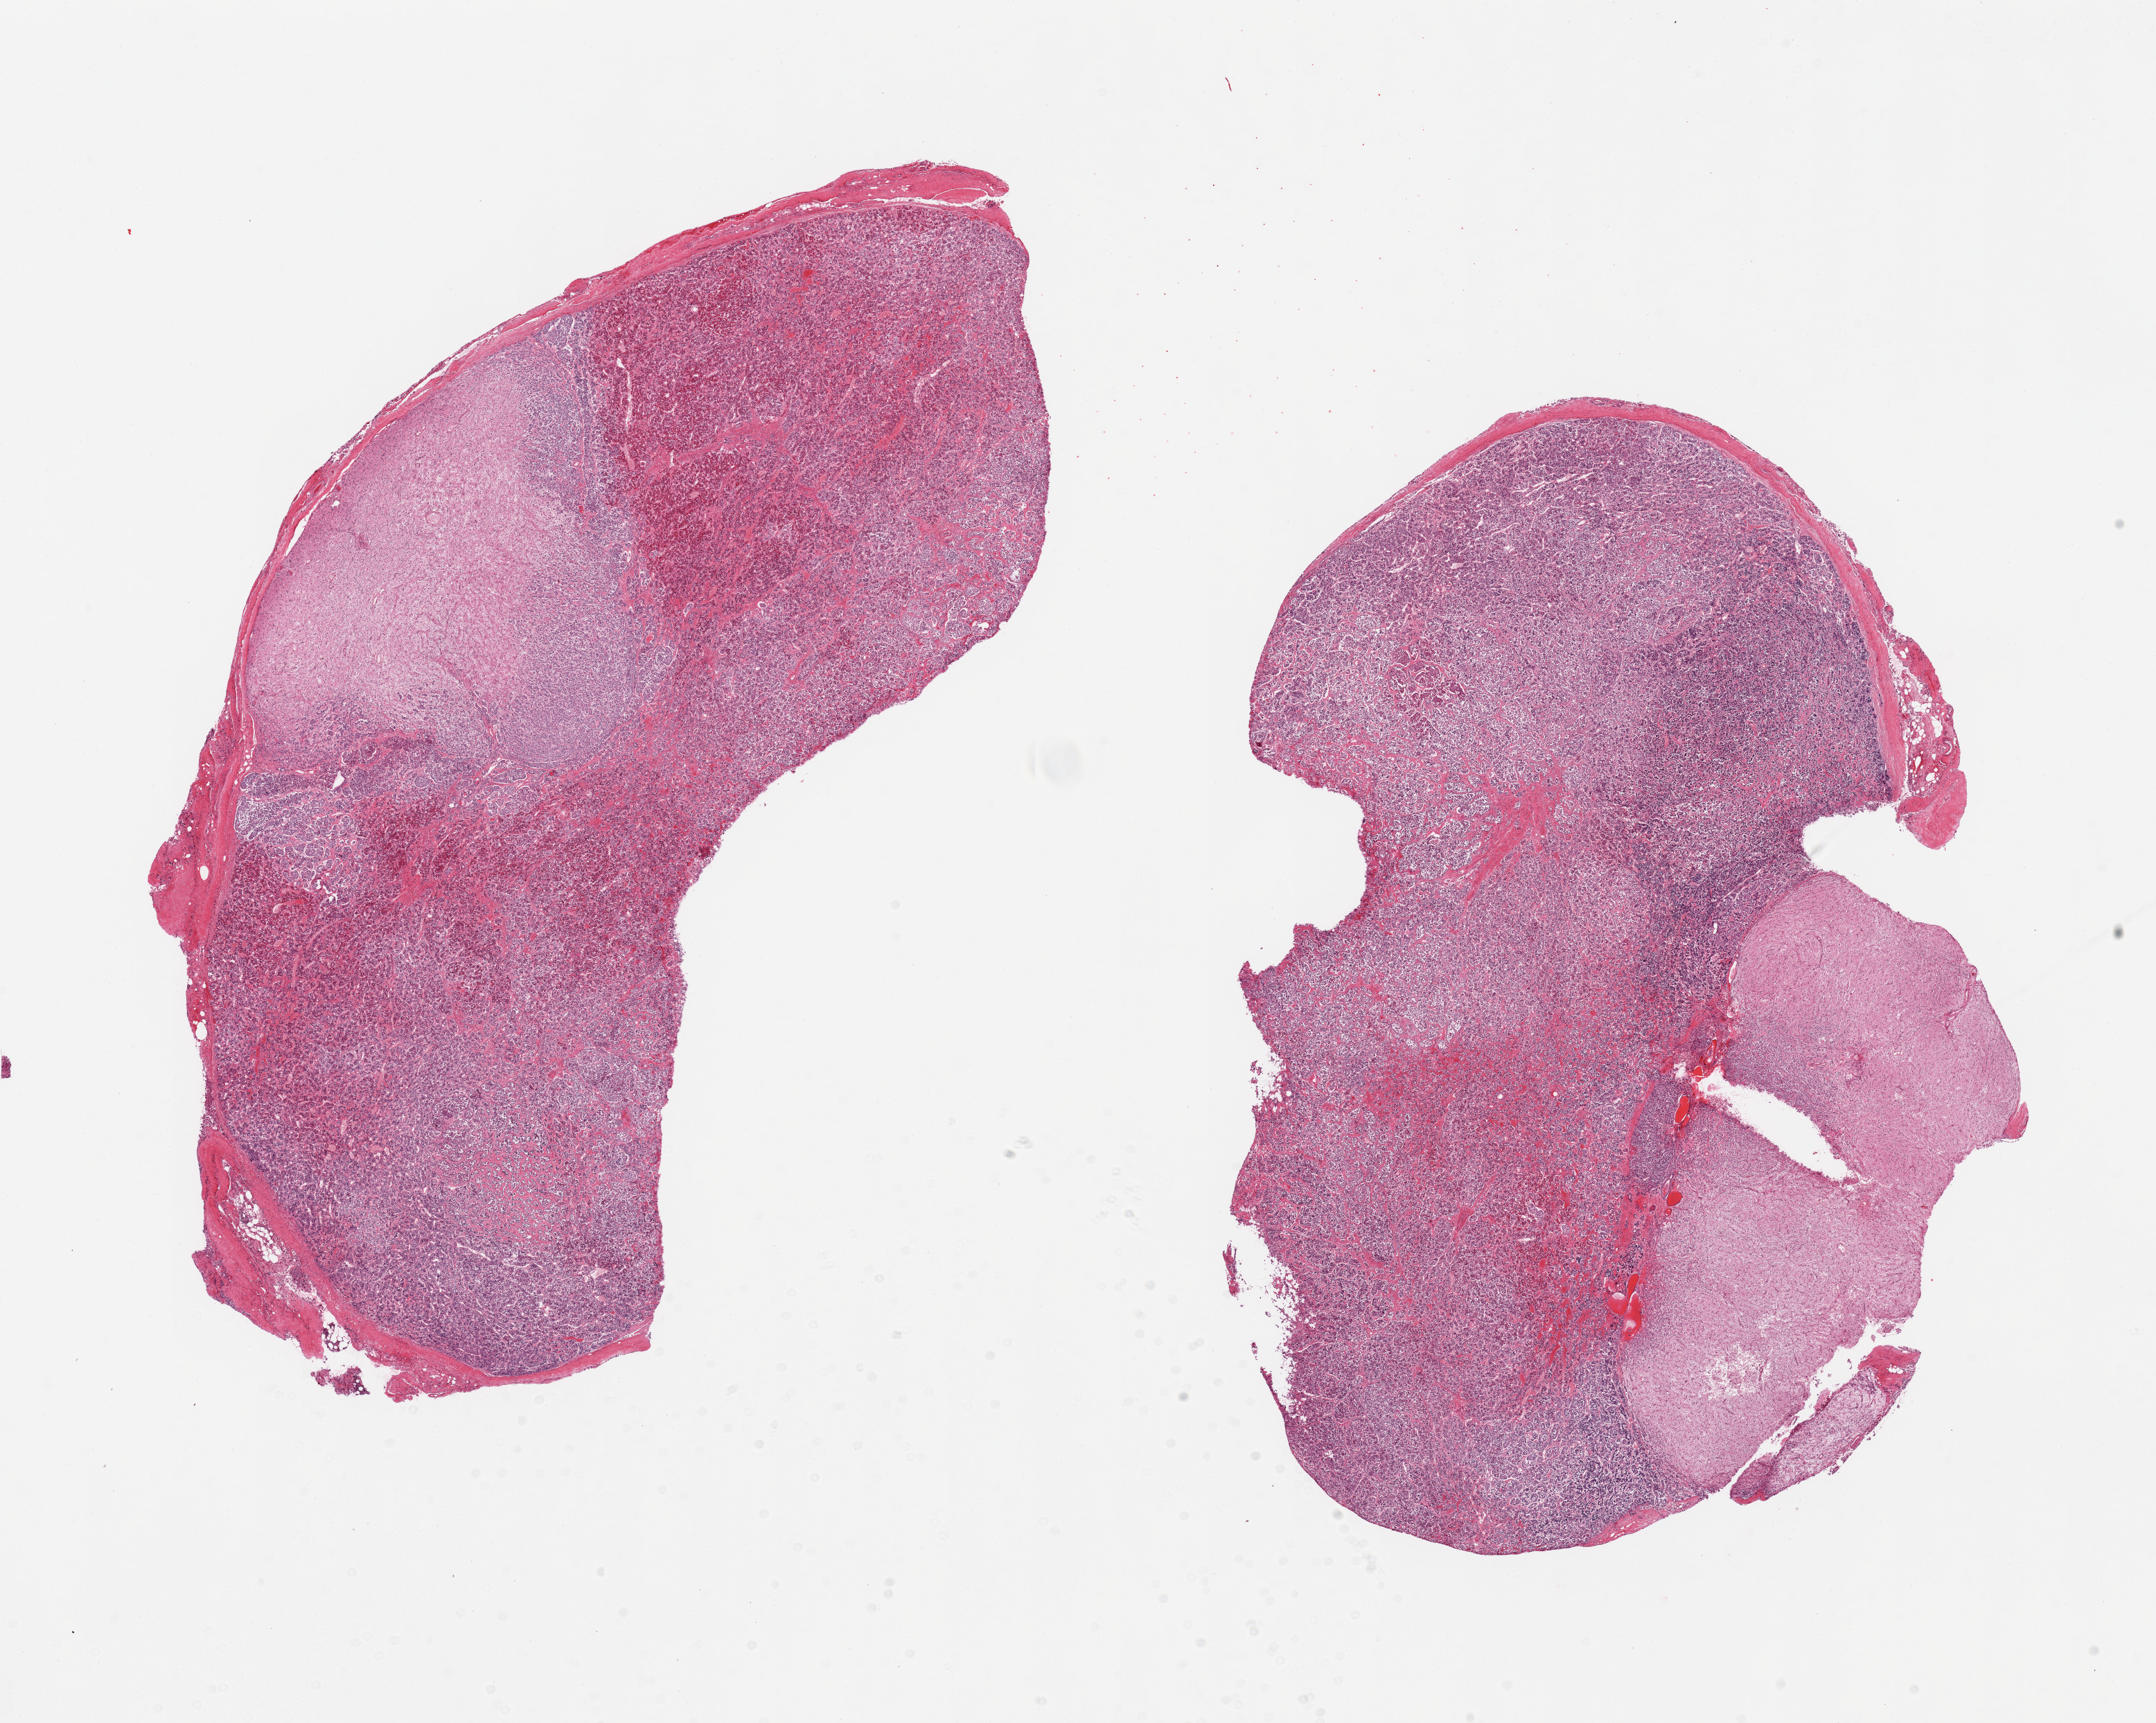
Digitized haematoxylin and eosin-stained section — low-resolution overview of the scanned area, about 24.6 x 19.7 mm; PAXgene-fixed paraffin-embedded (PFPE) section; section of pituitary (target tissue); tissue donor sample. Donor: male.
Reviewer comment on this tissue sample: 2 pieces, adenohypophysis and neurohypophysis with small portion of pars intermedia.